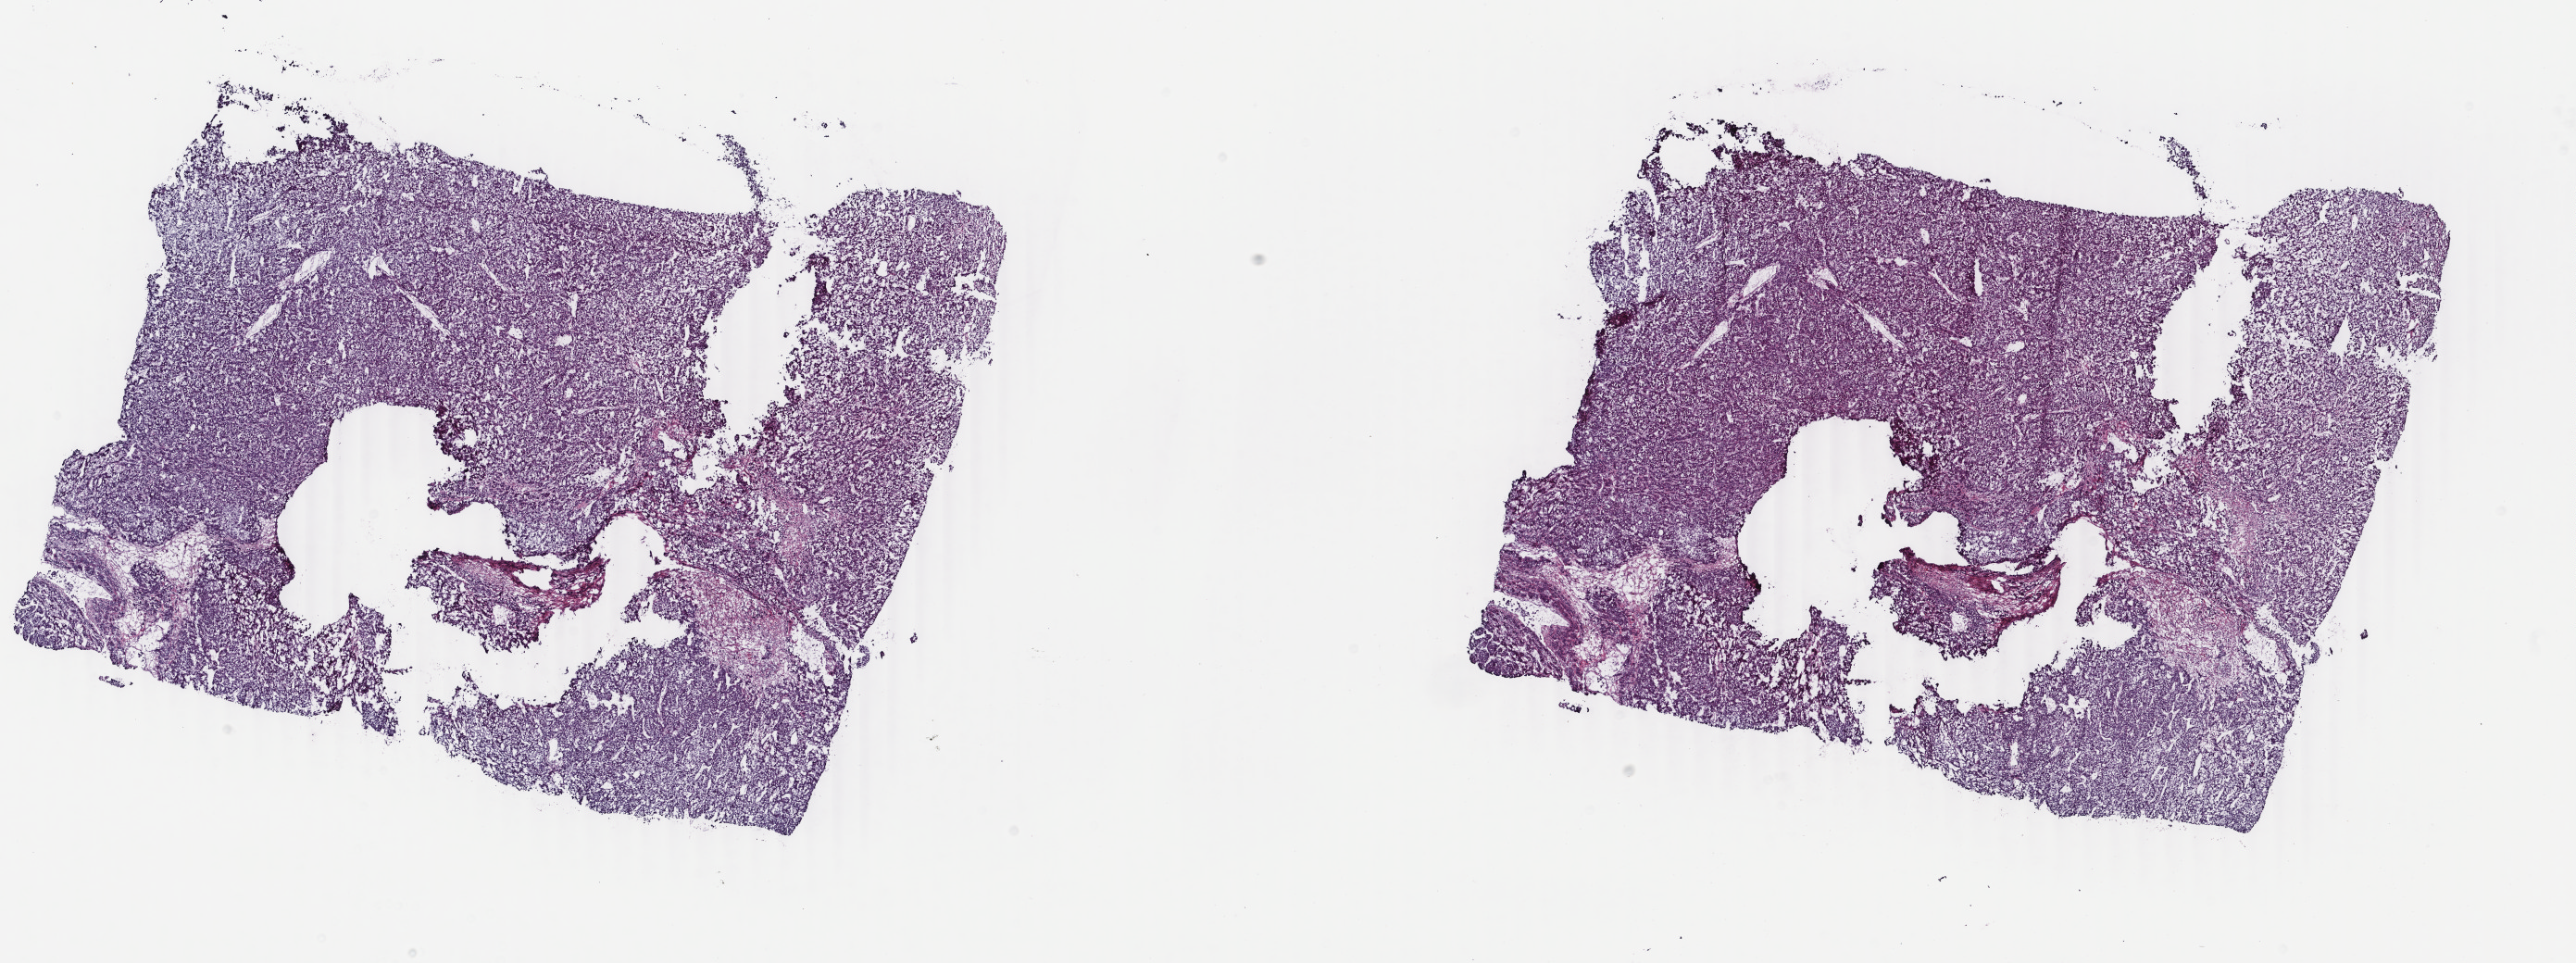
Digitized Hematoxylin and eosin (H&E) stained tissue section (whole slide) — shown as a low-resolution overview of the whole scanned area (about 22.1 x 8.3 mm, from a 40x scan), frozen section from the bottom of the tissue portion, liver, primary tumour sample. Female patient; age at initial diagnosis 57 years. Histologic grade: G2 (moderately differentiated). Pathologist review of this section (percent, as recorded): tumour cells 75%, tumour nuclei 75%, normal cells 0%, stromal cells 25%, necrosis 0%. Infiltration values recorded for this section: lymphocyte infiltration 5%, monocyte infiltration 0%, neutrophil infiltration 0%.
Pathologic diagnosis: Hepatocellular carcinoma, NOS. AJCC pathologic stage: I.